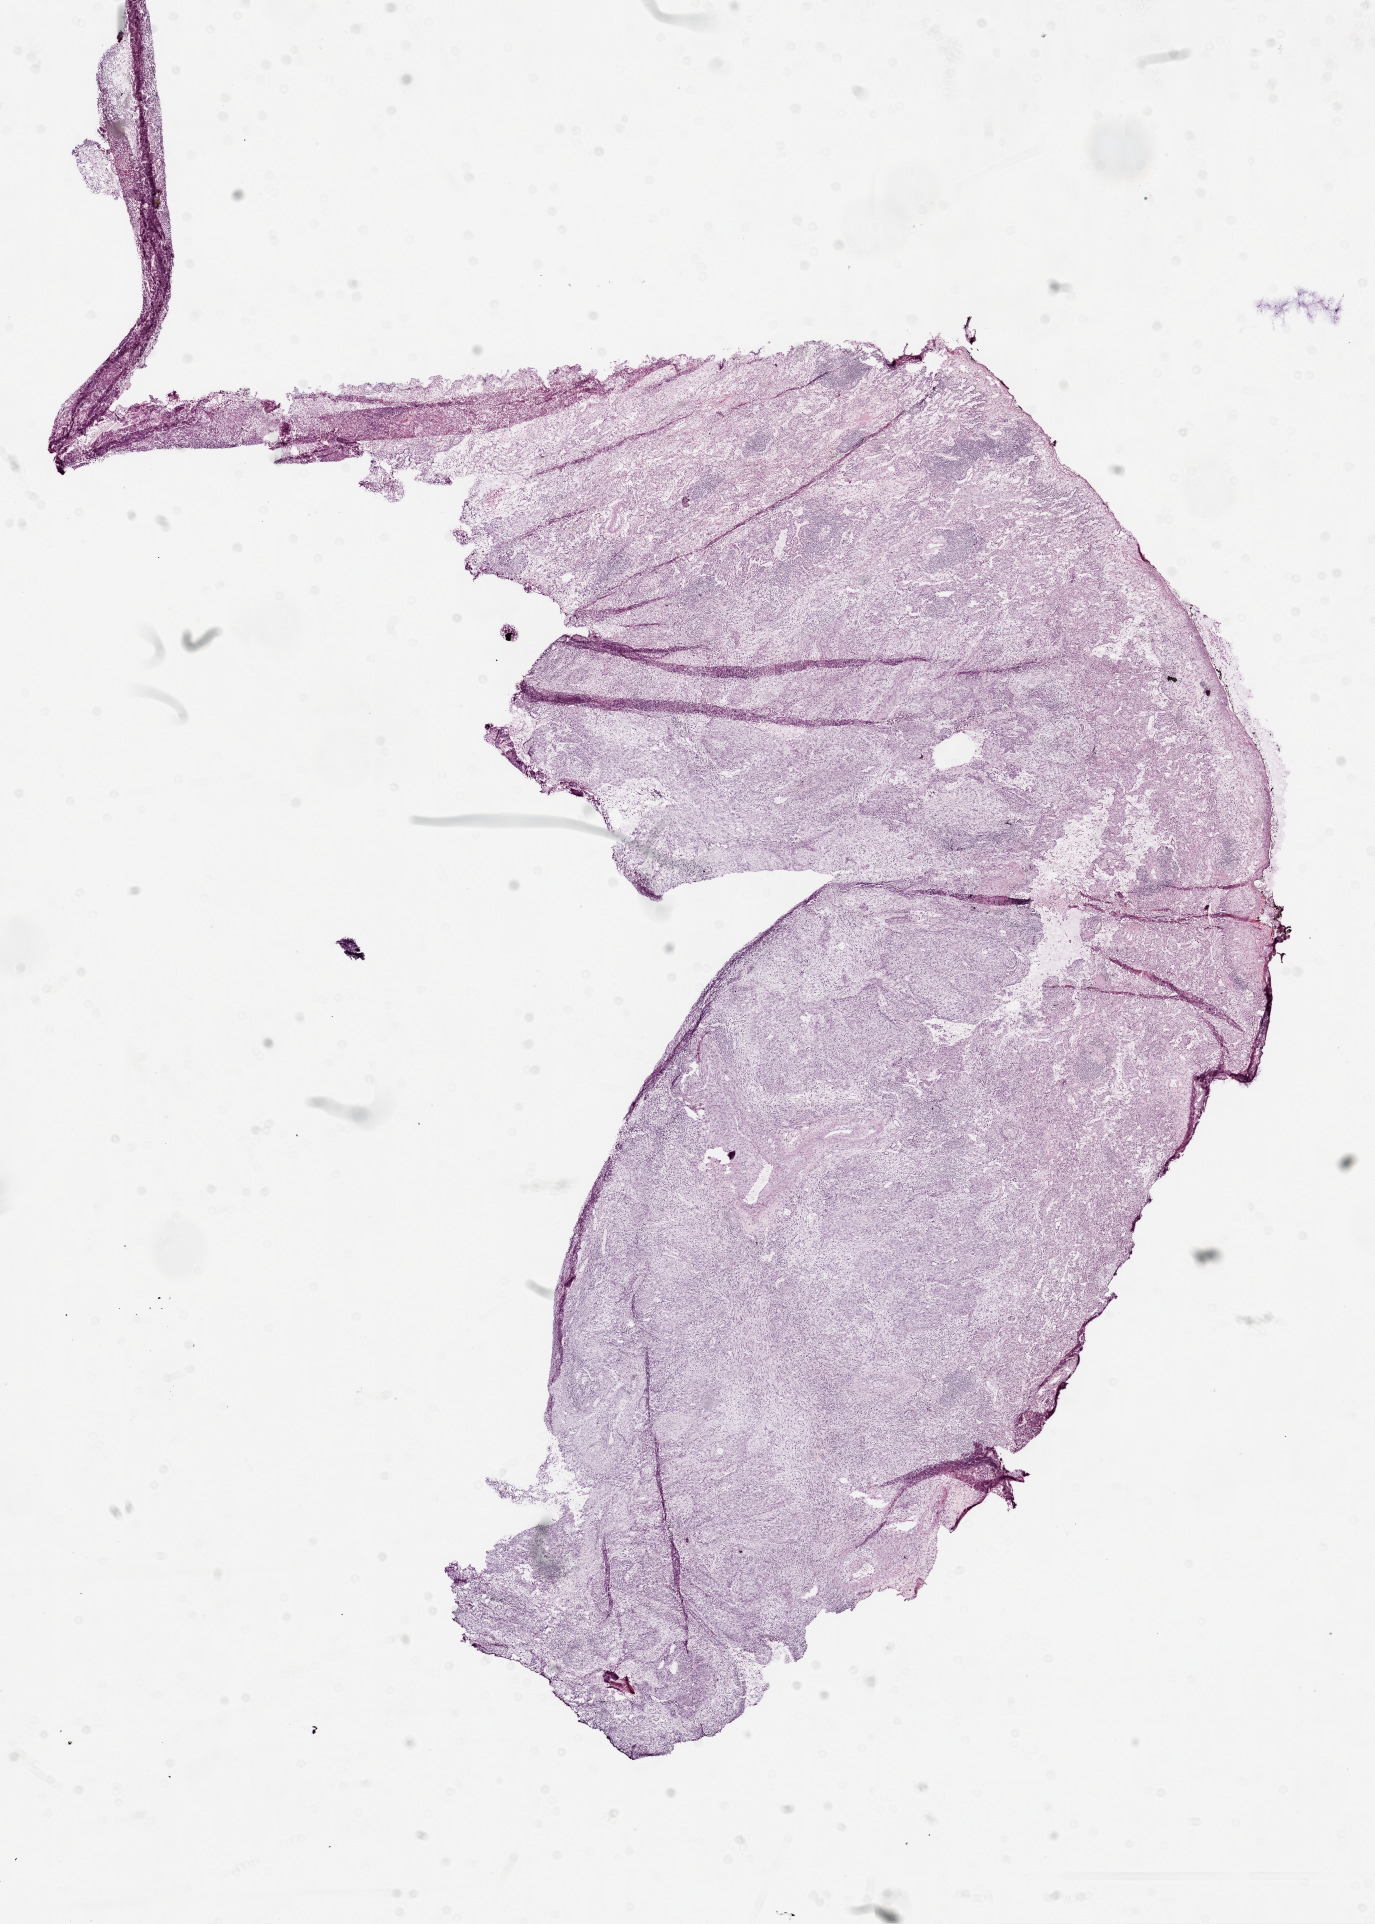
Hematoxylin and eosin (H&E) stained whole-slide image, a low-resolution overview of the entire scanned area, about 11.0 x 15.4 mm (acquisition: 20x scan). Frozen section. Sample: primary tumour, lung. Female, age 60 years at initial diagnosis. Pathologist review of this section (percent, as recorded): tumour cells 75%, tumour nuclei 75%, normal cells 0%, stromal cells 20%, necrosis 5%.
AJCC pathologic stage: IB. Histologic diagnosis: Squamous cell carcinoma, NOS (lower lobe, lung). Laterality: right.